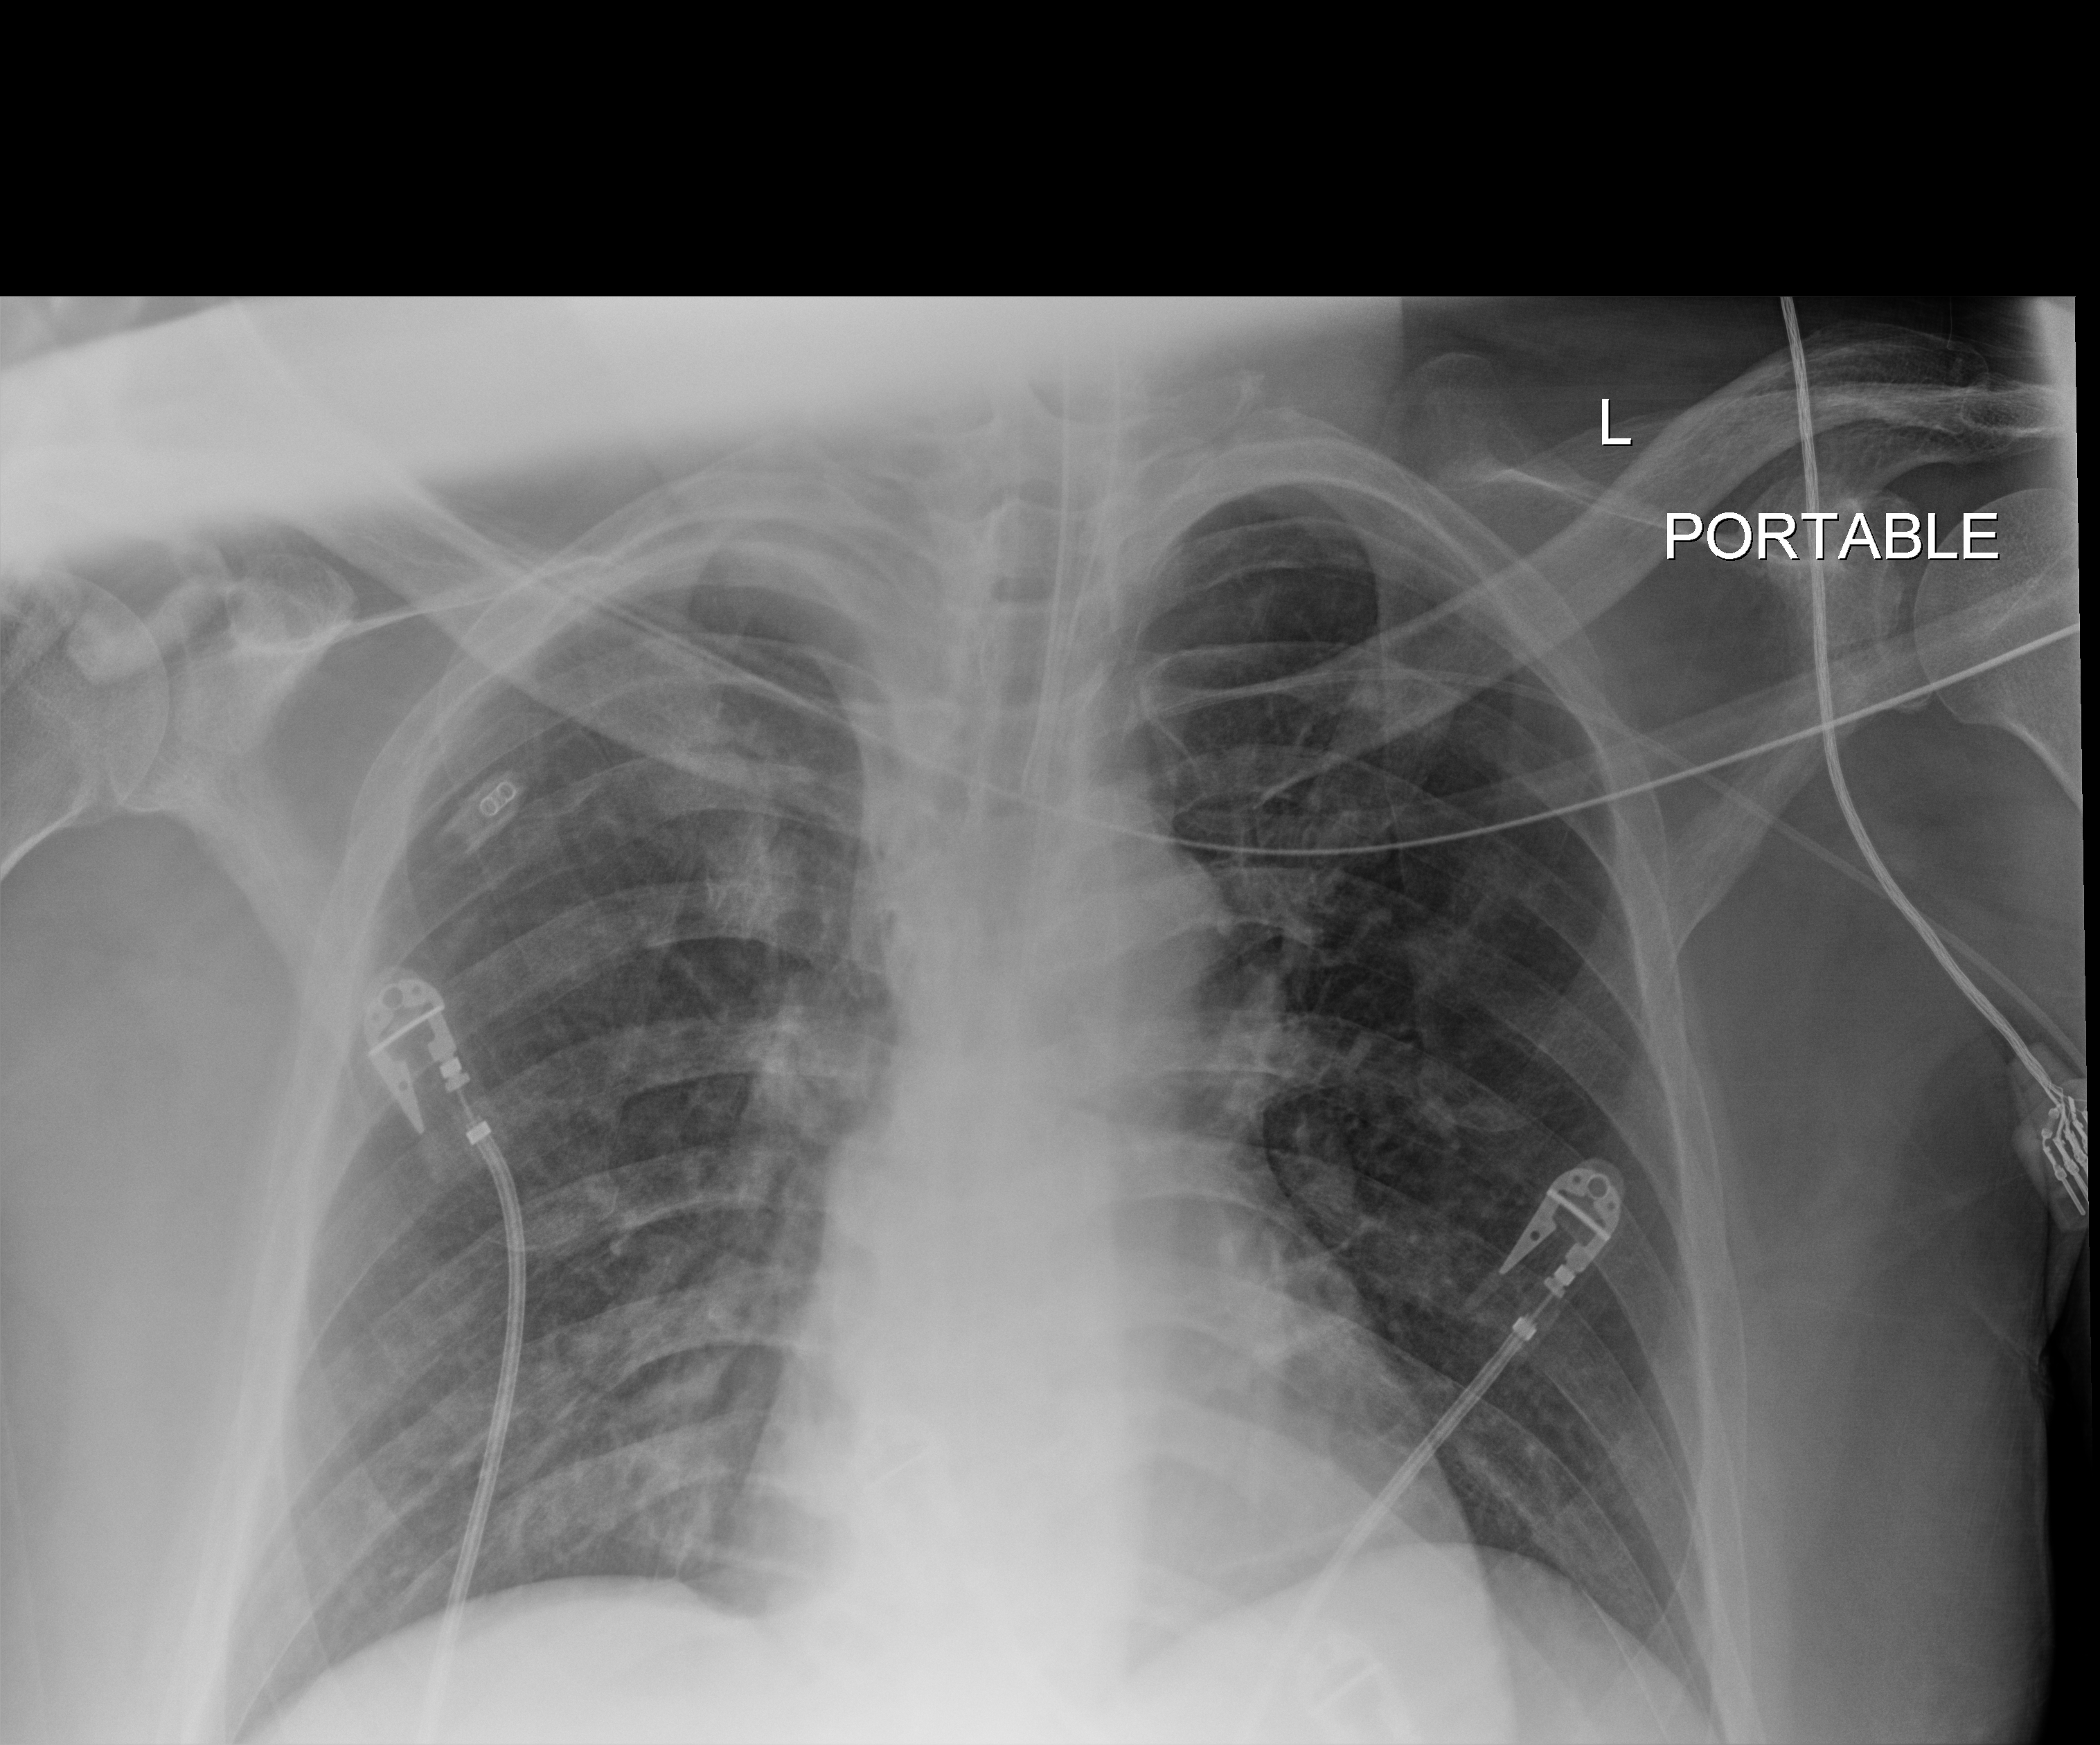
Bedside chest radiograph (digital radiography); anteroposterior (AP) projection. Patient hospitalised with COVID-19, aged 18–59 years.
Hospital-stay facts (about this admission, not read from this image; timing relative to this image not recorded):
- diabetes (admission record): yes